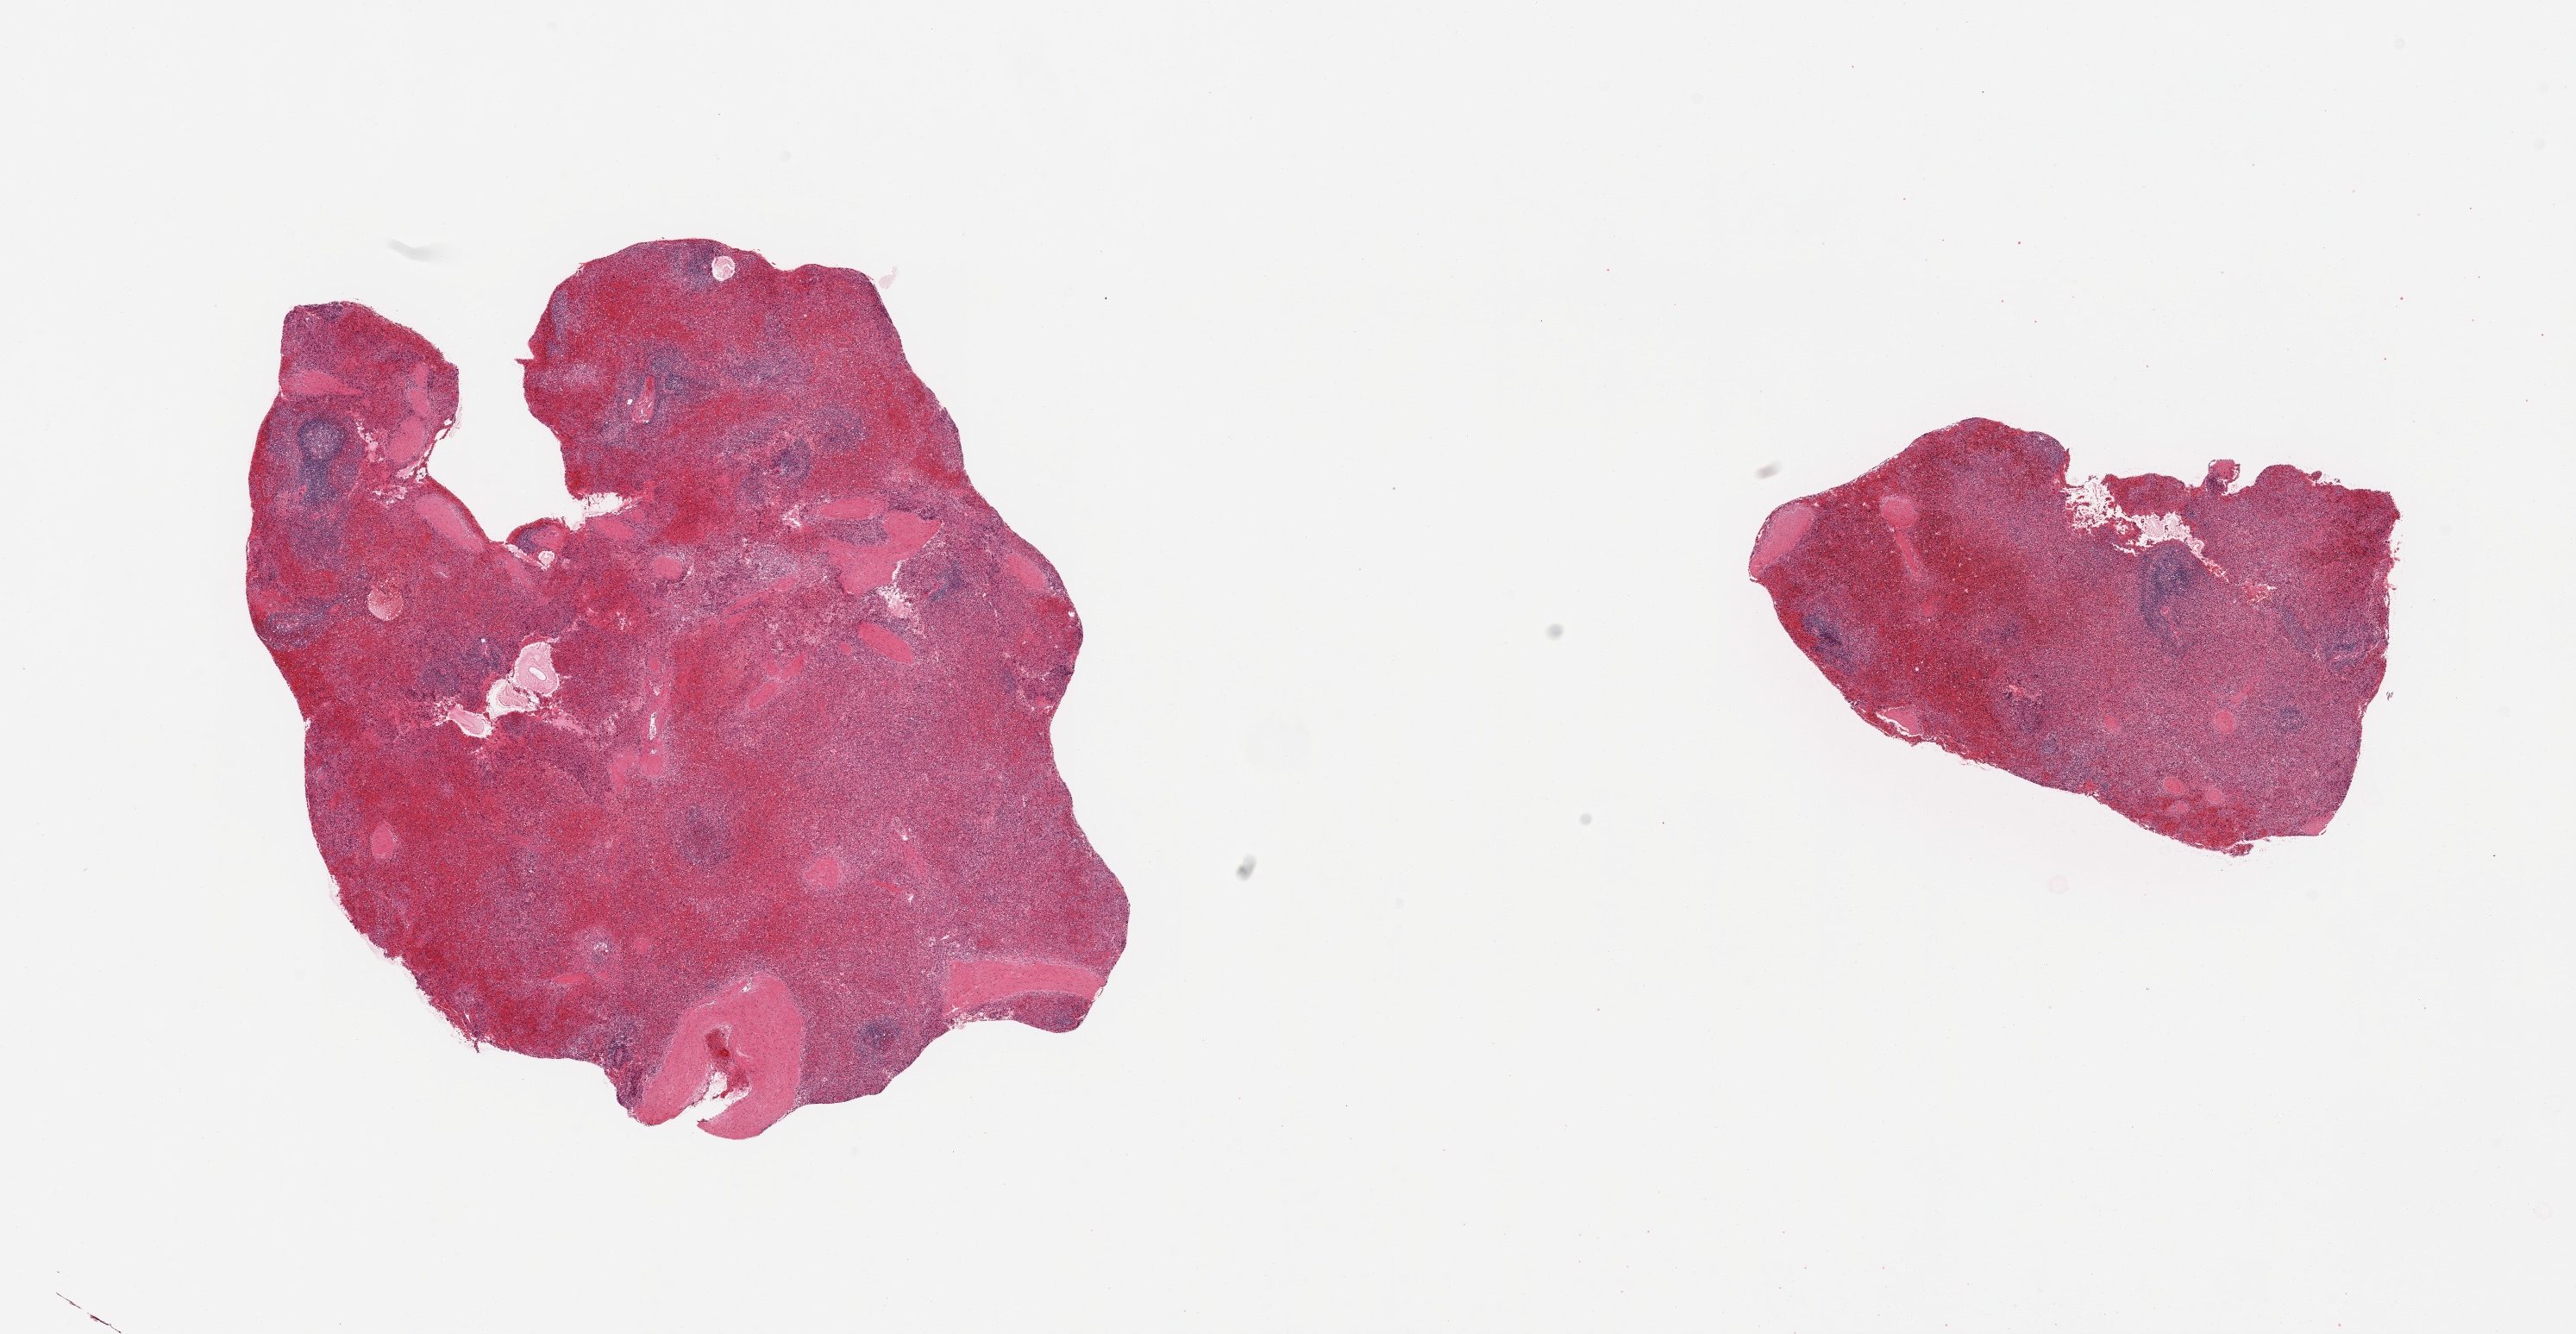
H&E whole-slide image, low-resolution overview of the scanned area, about 23.6 x 12.2 mm, PAXgene-fixed paraffin-embedded (PFPE) section, sampled site (target tissue): spleen, donor tissue sample.
Reviewer comment on this tissue sample: 2 pieces; moderately congested.